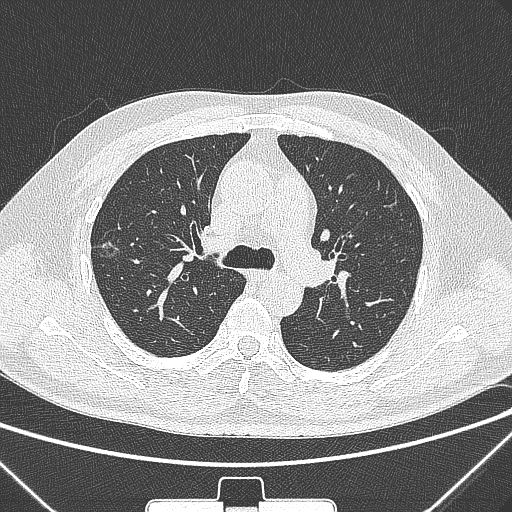
Chest CT, one axial slice; position 203 of 320 along the scan axis; lung window (W 1500 / L -600 HU); 1 mm slice thickness; 512 × 512 image matrix, field of view 350 × 350 mm. Patient: male, 58 years. Case-level facts recorded for this patient, not image findings: clinical TNM (as recorded): T1c N0 M0; histopathological grade: G2.
Annotated regions visible in this slice (rectangle marked by the reading radiologist):
- lung tumour (recorded histology: adenocarcinoma): bounding box <100,230,130,270> (left, top, right, bottom; pixels)